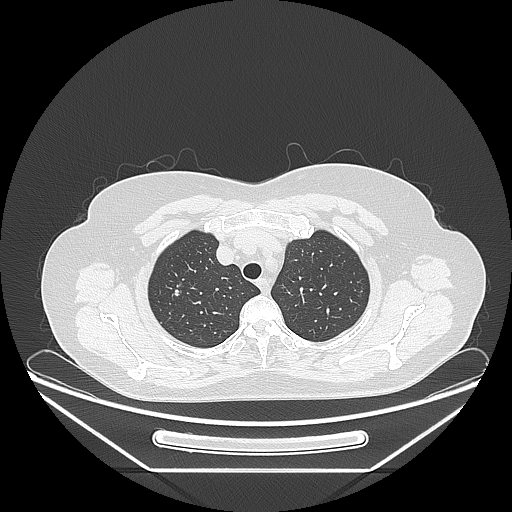
Chest CT, one axial slice. Position 202 of 236 along the scan axis. 120 kVp. Lung window (W 1500 / L -600 HU). 512 × 512 image matrix, field of view 433 × 433 mm. Patient: female, 60 years. Case-level facts recorded for this patient, not image findings: clinical TNM (as recorded): T1c N0 M0; histopathological grade: G2-3.
Annotated regions visible in this slice (rectangle marked by the reading radiologist):
- lung tumour (recorded histology: adenocarcinoma): box from (x=169, y=277) to (x=182, y=310) px